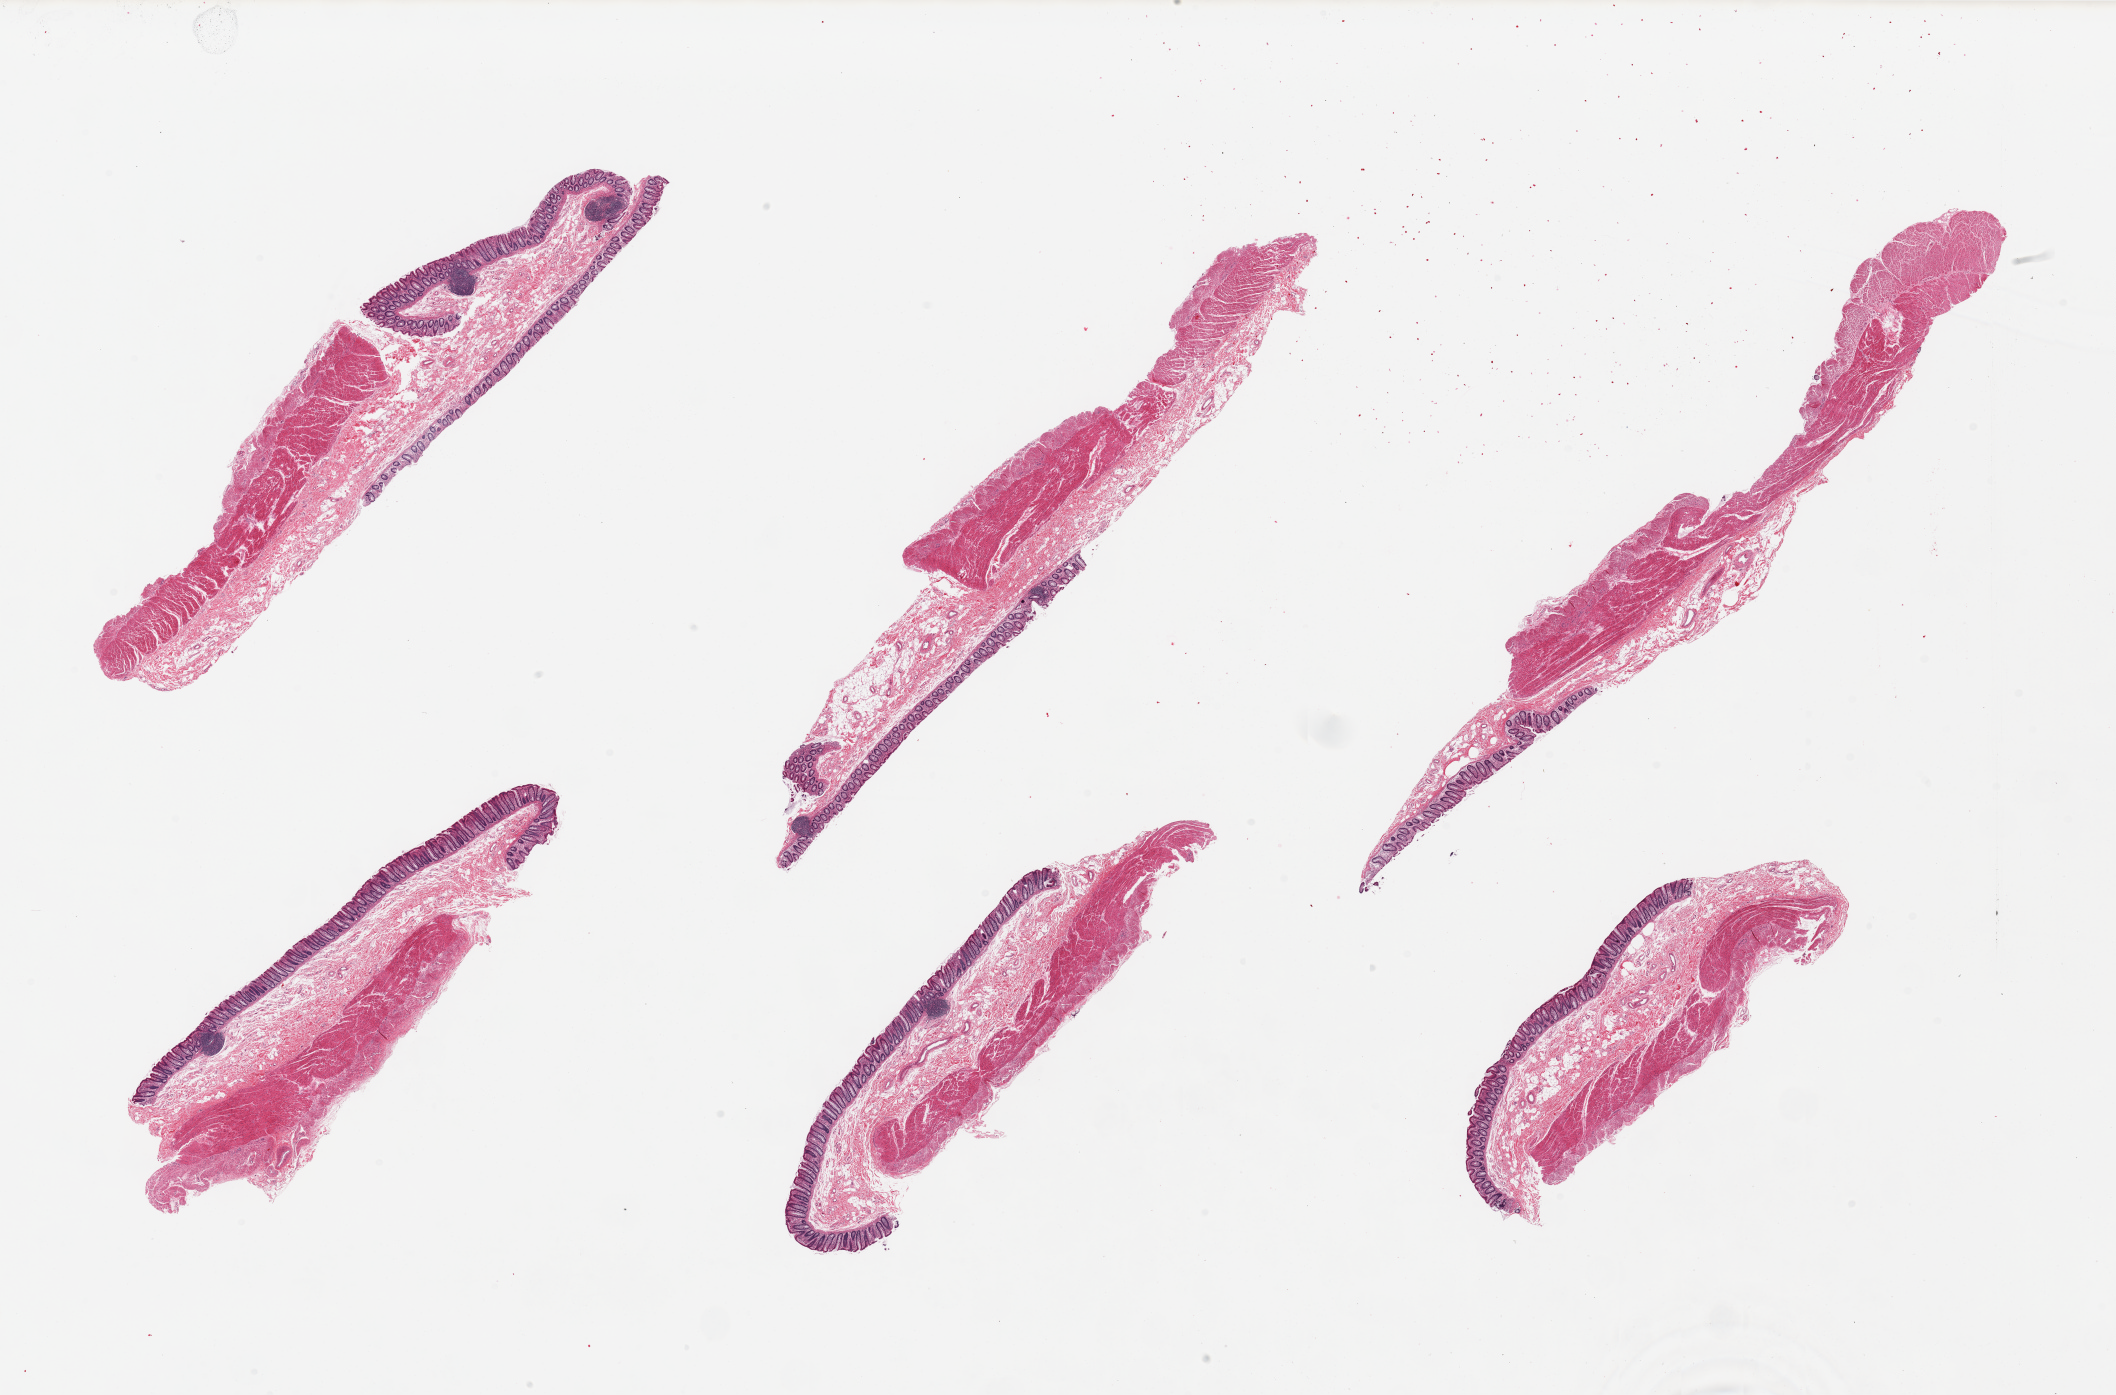
H&E whole-slide image, brightfield, a low-resolution overview of the entire scanned area, about 33.5 x 22.1 mm (acquisition: 20x scan). PAXgene-fixed, paraffin-embedded tissue. Section of transverse colon (target tissue). Tissue donor sample. Donor sex: female.
Reviewer comment on this tissue sample: 6 pieces, mucosa fairly well preserved, ~0.3mm, ~10-15% thickness.